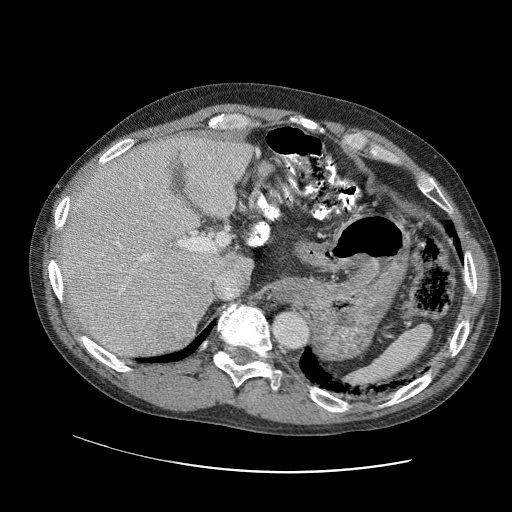
Contrast-enhanced abdominal CT (liver protocol), one axial slice. Position 73 of 109 along the scan axis. Soft-tissue window (W 400 / L 40 HU). 2.5 mm slice thickness. 512 × 512 image matrix, field of view 400 × 400 mm. From the clinical record (not read from this slice): diagnosis: hepatocellular carcinoma (patient treated with transarterial chemoembolisation; whether this scan precedes or follows treatment is not stated here); TNM stage (as recorded): Stage-IIIC; Child-Pugh class: B.
Annotated regions visible in this slice (semi-automatically segmented with operator editing):
- liver parenchyma outside the tumour (the mass and vessels are separate outlines, so this box may not span the whole liver): box from (x=56, y=132) to (x=250, y=358) px
- mass: (x=159, y=316)–(x=194, y=348)
- liver vessels: (x=97, y=152)–(x=246, y=330)